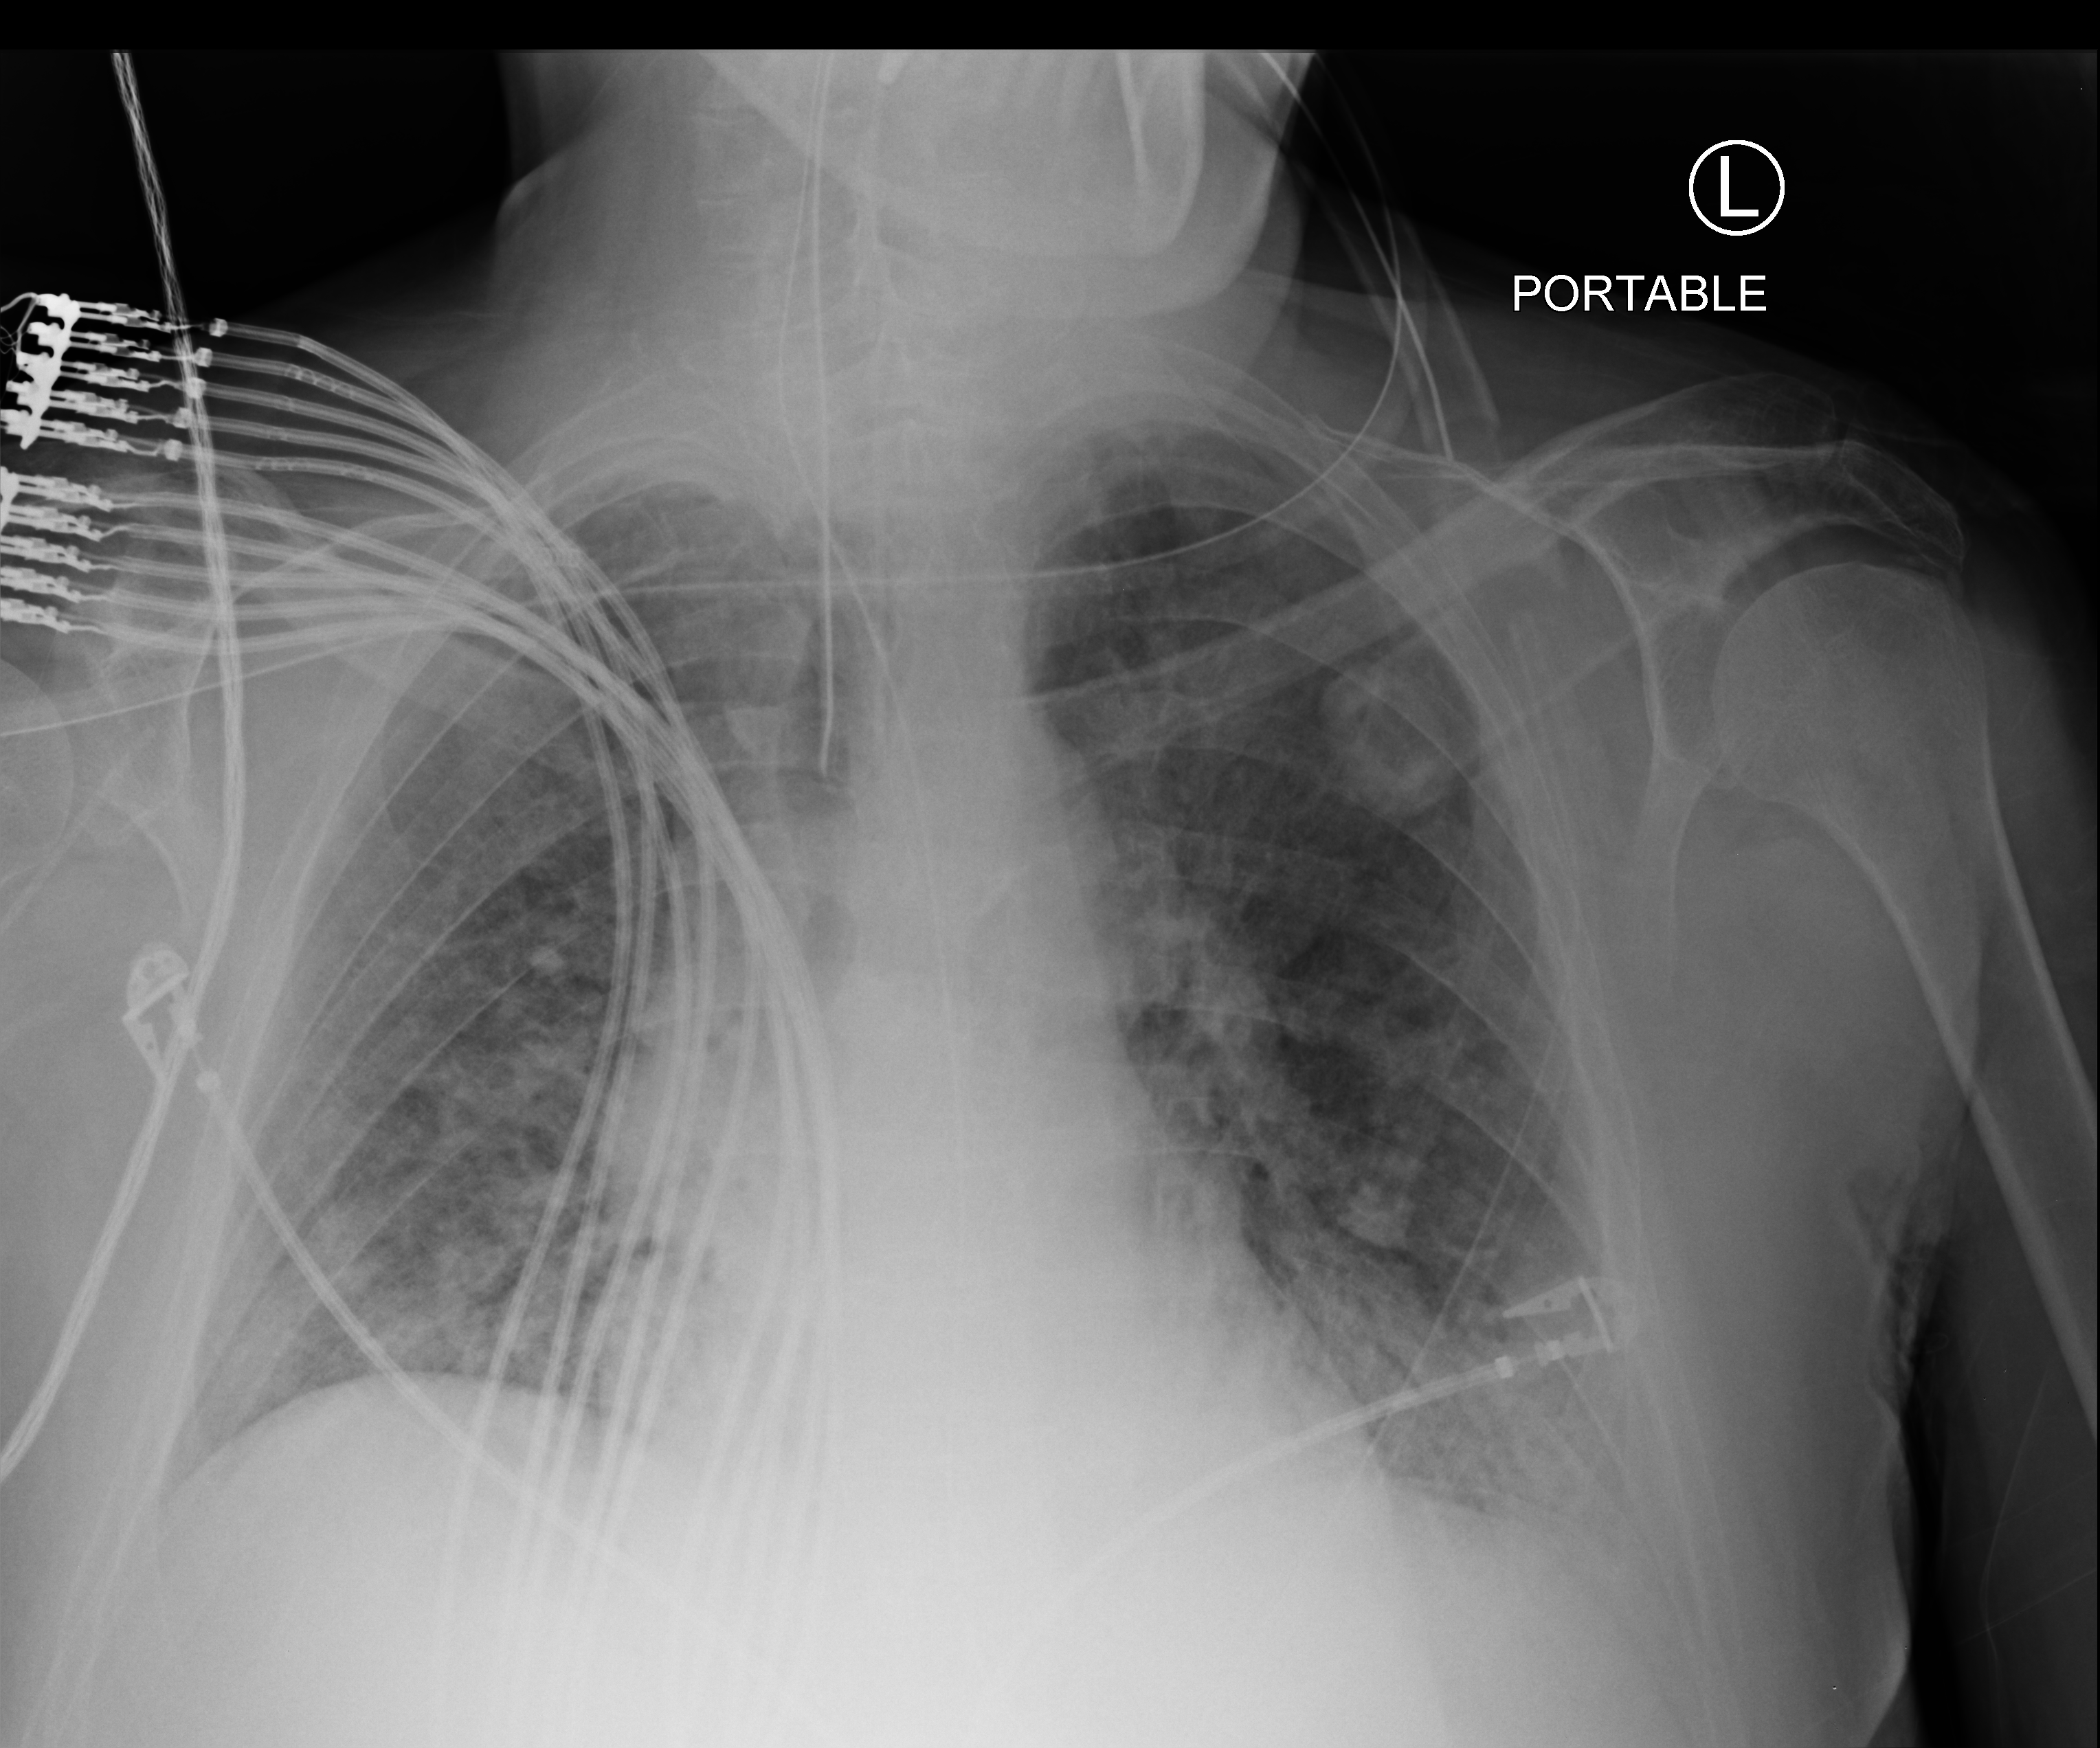
Portable chest radiograph. Male patient hospitalised with COVID-19, age 60–74 years.
Admission-level facts for this patient (not findings on this image; timing relative to this image not recorded): diabetes (admission record): no; mechanically ventilated during this hospital stay: yes; admitted to intensive care during this hospital stay: yes.